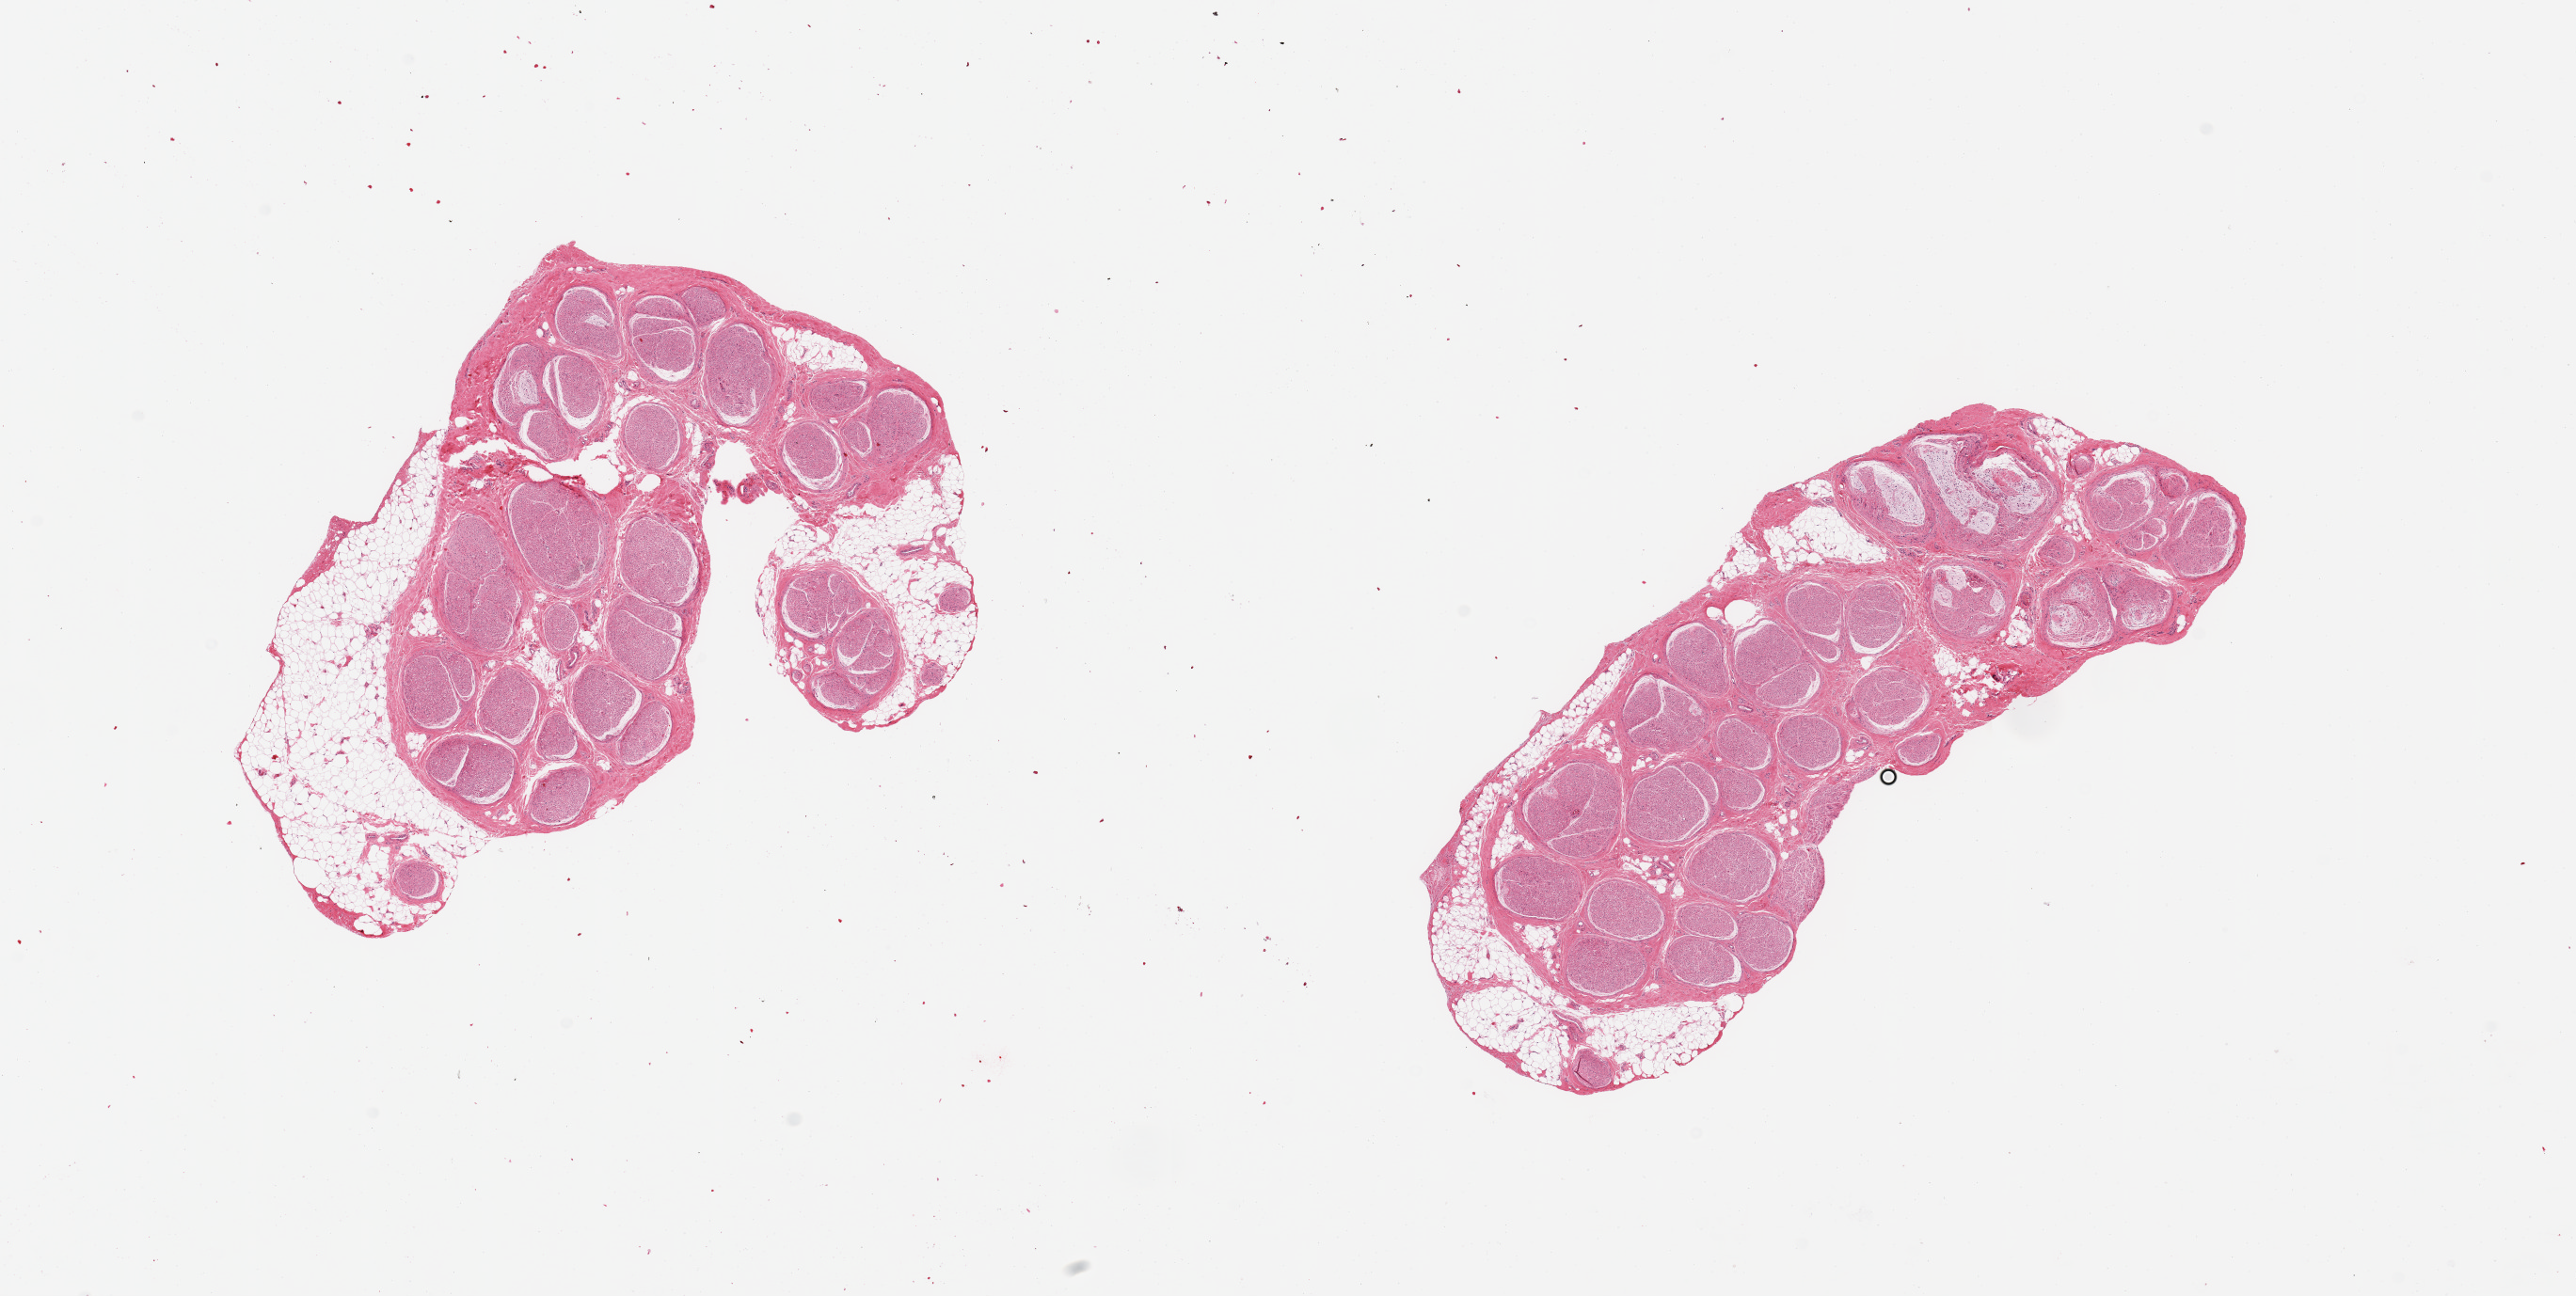
H&E whole-slide image, low-resolution overview of the scanned area, about 21.7 x 10.9 mm (slide scanned at 20x); PAXgene-fixed paraffin-embedded (PFPE) section; target tissue: tibial nerve; donor tissue sample.
Review note (as recorded): 2 pieces; 30% external fat.